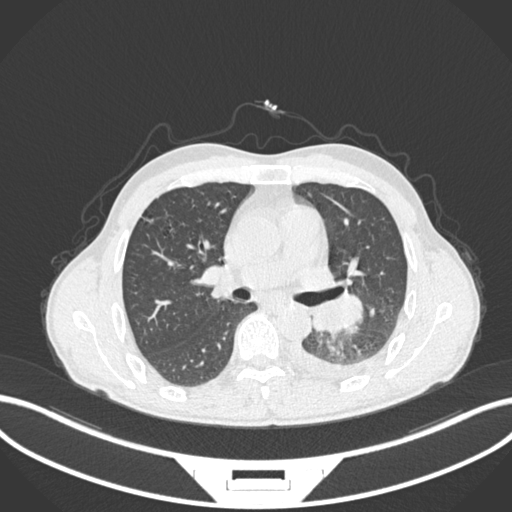
Chest CT, one axial slice; position 144 of 222 along the scan axis; reconstruction kernel B30f; lung window (W 1500 / L -600 HU); 512 × 512 image matrix. Male patient, age 47 years. Case-level facts recorded for this patient, not image findings: clinical TNM (as recorded): T3 N1 M1c.
Outlined on this slice (bounding box drawn by a radiologist):
- lung tumour (recorded histology: small cell carcinoma): box from (x=309, y=293) to (x=368, y=334) px